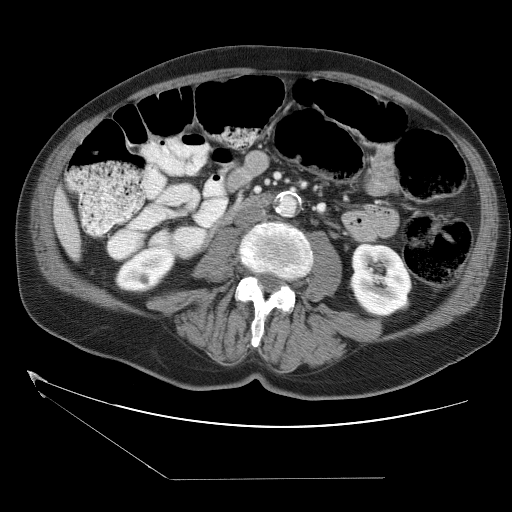
Contrast-enhanced abdominal CT (liver protocol), one axial slice. Slice 1 of 38 in the series (ordered by position). Soft-tissue window (W 400 / L 40 HU). 5 mm slice thickness. 512 × 512 image matrix. From the clinical record (not read from this slice): diagnosis: hepatocellular carcinoma (patient treated with transarterial chemoembolisation; whether this scan precedes or follows treatment is not stated here); TNM stage (as recorded): Stage-II; Child-Pugh class: A; tumour differentiation: moderately differentiated; tumour size: 0.8 cm.
Annotated regions visible in this slice (semi-automatically segmented with operator editing):
- liver parenchyma outside the tumour (the mass and vessels are separate outlines, so this box may not span the whole liver): bounding box <54,190,80,258> (left, top, right, bottom; pixels)